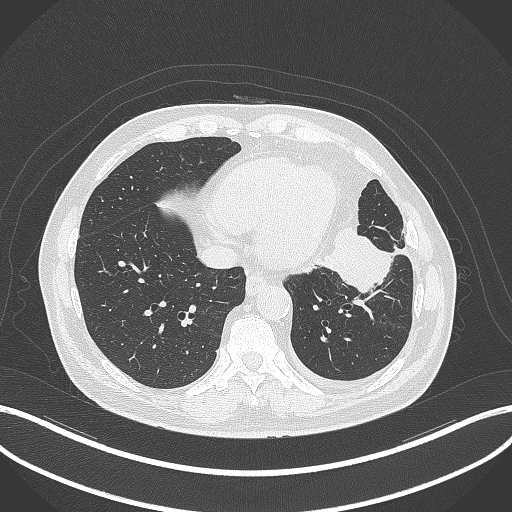
Chest CT, one axial slice. Position 107 of 230 along the scan axis. Lung window (W 1500 / L -600 HU). 1 mm slice thickness. 512 × 512 image matrix, field of view 400 × 400 mm. Patient: male, 68 years. From the clinical record (not read from this slice): clinical TNM (as recorded): T2b N0 M0.
Structures marked on this image (bounding box drawn by a radiologist):
- lung tumour (recorded histology: squamous cell carcinoma): bounding box (x1, y1, x2, y2) in pixels: (315, 222, 394, 293)